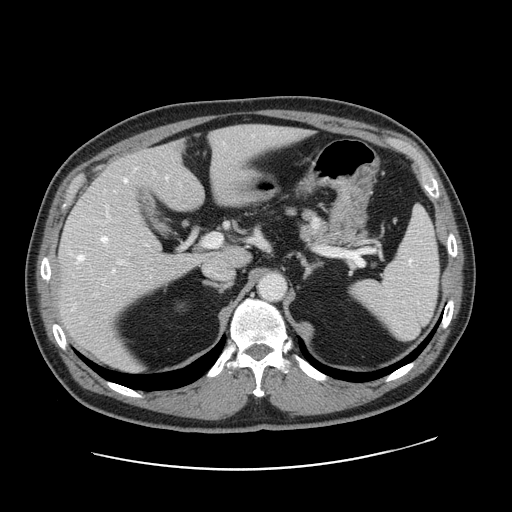
Contrast-enhanced abdominal CT, one axial slice; slice 101 of 178 in the series (ordered by position); intravenous contrast given; soft-tissue window (W 400 / L 40 HU); 512 × 512 image matrix, field of view 403 × 403 mm. Male patient, age 63 years. Case-level facts recorded for this patient, not image findings: diagnosis: colorectal cancer liver metastases, imaged before liver resection; multiple liver metastases: yes; largest metastasis: 8 cm; disease in both lobes: yes.
Outlined on this slice (expert manual segmentation):
- hepatic veins: bounding box [x1, y1, x2, y2] px = [78, 178, 127, 270]
- liver: [59, 125, 299, 368]
- planned liver remnant (the part of the liver to remain after resection): [120, 125, 298, 264]
- portal vein (with intrahepatic branches): [119, 234, 222, 263]